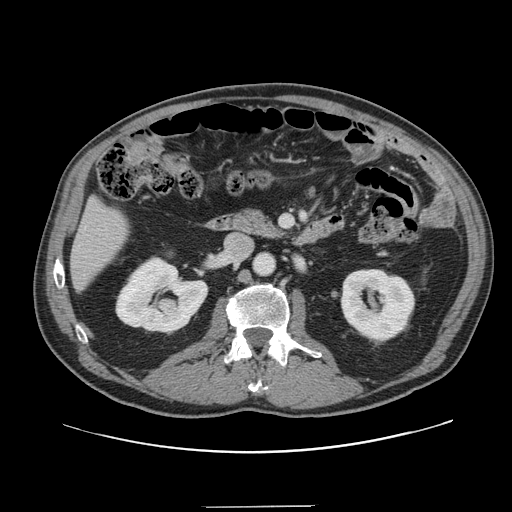
Contrast-enhanced abdominal CT, one axial slice; slice 57 of 139 in the series (ordered by position); intravenous contrast given; soft-tissue window (W 400 / L 40 HU); 512 × 512 image matrix. Male patient, age 64 years. Case-level facts recorded for this patient, not image findings: diagnosis: colorectal cancer liver metastases, imaged before liver resection; multiple liver metastases: yes; largest metastasis: 3.5 cm; disease in both lobes: yes.
Outlined on this slice (outlined manually by an expert reader):
- liver: box from (x=72, y=201) to (x=127, y=287) px
- planned liver remnant (the part of the liver to remain after resection): (x=72, y=201)–(x=128, y=287)